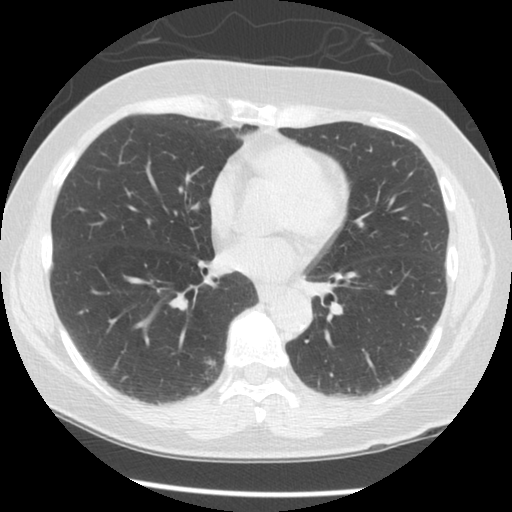
Low-dose screening chest CT, one axial slice; slice 60 of 125 in the series (ordered by position); reconstruction kernel STANDARD; lung window (W 1500 / L -600 HU); 512 × 512 image matrix, field of view 331 × 331 mm.
Outlined on this slice (expert manual segmentation):
- lesion 1 (tumor, lower lobe of right lung): box from (x=206, y=360) to (x=216, y=368) px